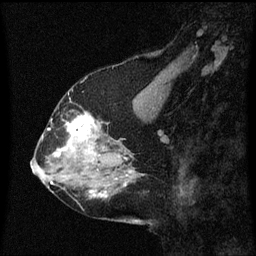
Breast MRI (dynamic contrast-enhanced), one sagittal slice. Position 25 of 60 along the scan axis. Dynamic contrast-enhanced series, image 2 of 3 at this slice position (ordered by acquisition). 1.5 T. TE 4.2 ms, TR 8.4 ms. 256 × 256 image matrix, field of view 200 × 200 mm. Female patient, age 58 years.
Annotated regions visible in this slice (semi-automatically segmented with operator editing):
- analysis volume of interest (the breast-tissue region the enhancement analysis was run in; not a lesion): bounding box [x1, y1, x2, y2] px = [58, 112, 99, 151]
- tumour enhancement mask (voxels above the 70 % enhancement threshold inside the analysis volume of interest): [62, 112, 95, 151]